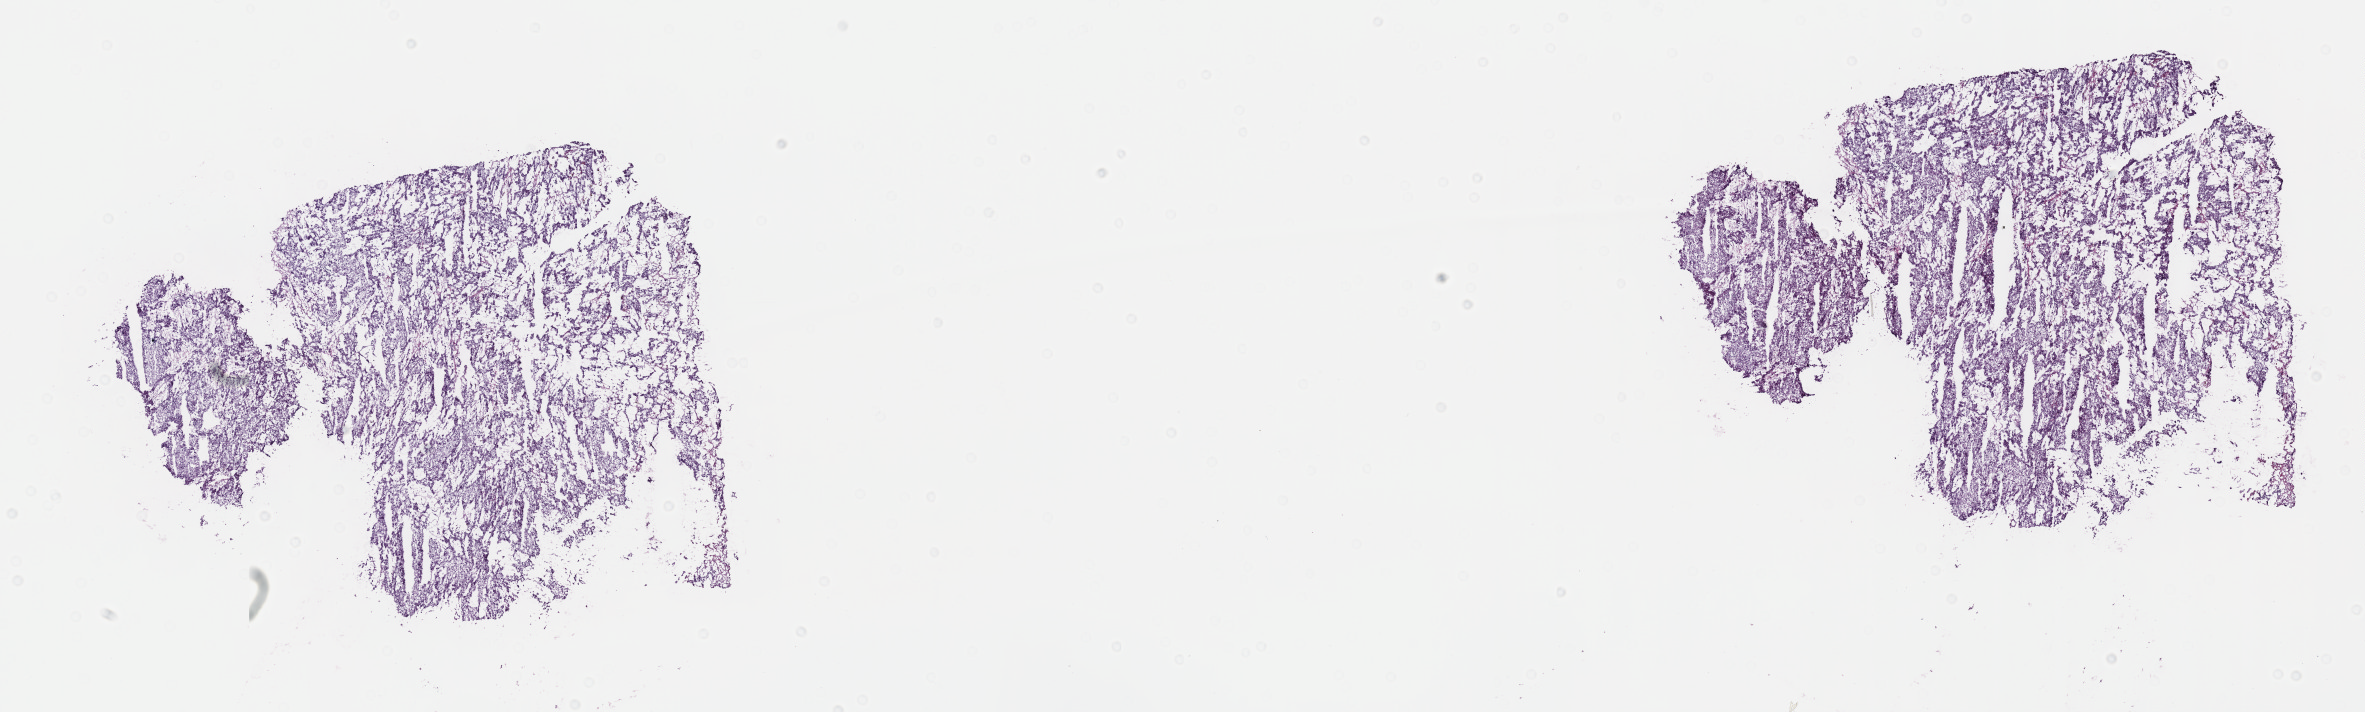
Whole-slide histology image, Hematoxylin and eosin (H&E) stained — shown as a low-resolution overview of the whole scanned area (about 19.1 x 5.8 mm, from a 40x scan). Frozen section from the top of the tissue portion. Primary tumour sample from the liver. Patient: female, age at initial diagnosis 54 years. Histologic grade: G1 (well differentiated). Slide review estimates, as recorded: tumour cells 100%, tumour nuclei 90%, normal cells 0%, stromal cells 0%, necrosis 0%. Infiltration values recorded for this section: lymphocyte infiltration 0%, monocyte infiltration 0%, neutrophil infiltration 0%.
* AJCC pathologic stage: I (6th edition)
* diagnosis: Hepatocellular carcinoma, NOS